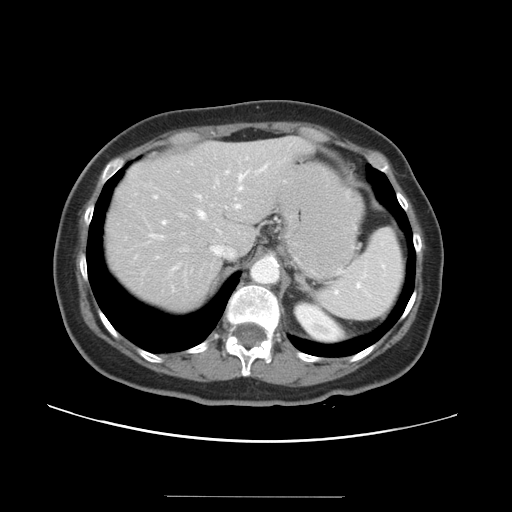
Contrast-enhanced abdominal CT, one axial slice; position 26 of 34 along the scan axis; reconstruction kernel STANDARD; 120 kVp; intravenous contrast given; soft-tissue window (W 400 / L 40 HU); 5 mm slice thickness; 512 × 512 image matrix, field of view 382 × 382 mm. Female patient, age 69 years. From the clinical record (not read from this slice): diagnosis: colorectal cancer liver metastases, imaged before liver resection; multiple liver metastases: yes.
Outlined on this slice (expert manual segmentation):
- hepatic veins: box from (x=148, y=164) to (x=267, y=284) px
- liver: (x=106, y=137)–(x=310, y=312)
- planned liver remnant (the part of the liver to remain after resection): (x=106, y=137)–(x=310, y=312)
- portal vein (with intrahepatic branches): (x=163, y=221)–(x=165, y=224)